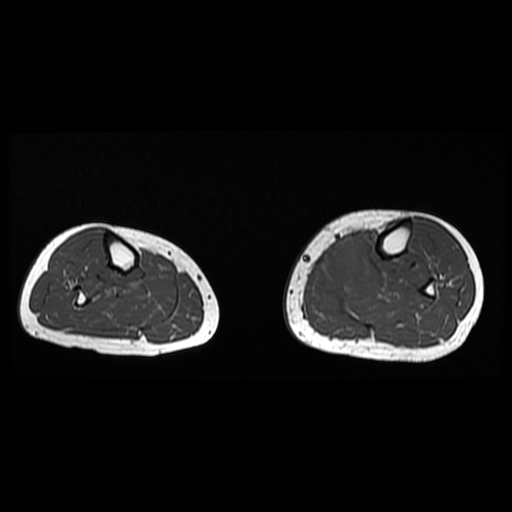
MRI of an extremity soft-tissue mass, one axial slice; position 10 of 38 along the scan axis; 512 × 512 image matrix, field of view 330 × 330 mm. Female patient. Case-level facts recorded for this patient, not image findings: histological type: extraskeletal high grade osteogenic sarcoma; grade: high; site of the primary tumour: left calf.
Annotated regions visible in this slice (manually delineated by an expert):
- gross tumour volume (mass): bounding box [x1, y1, x2, y2] px = [320, 242, 361, 289]